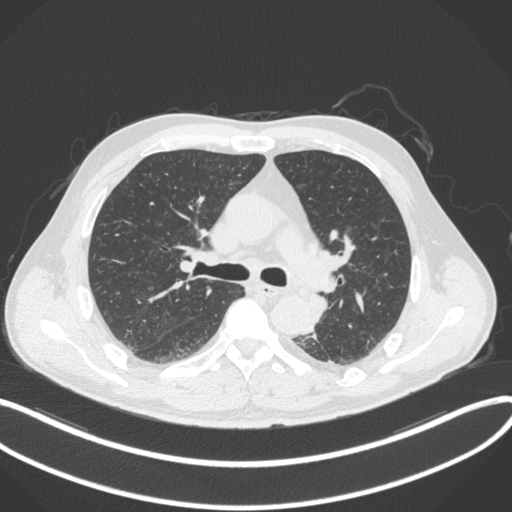
Chest CT, one axial slice. Slice 220 of 328 in the series (ordered by position). 120 kVp. Lung window (W 1500 / L -600 HU). 512 × 512 image matrix, field of view 400 × 400 mm. Male patient, age 59 years. Case-level facts recorded for this patient, not image findings: clinical TNM (as recorded): T2a N2 M0.
Structures marked on this image (bounding box drawn by a radiologist):
- lung tumour (recorded histology: squamous cell carcinoma): bounding box (x1, y1, x2, y2) in pixels: (309, 292, 330, 326)